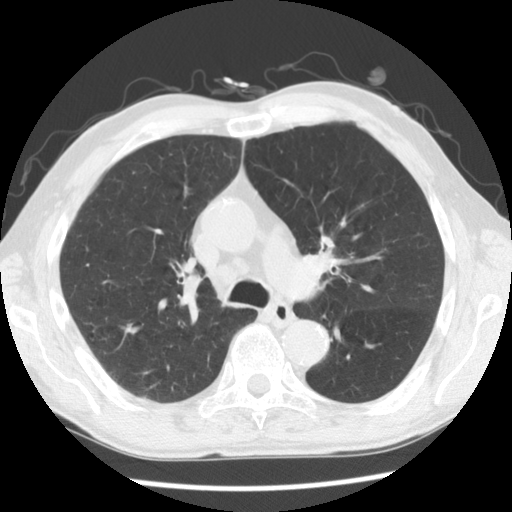
Low-dose screening chest CT, axial slice, baseline annual screen, lung window (W 1500 / L -600 HU), slice 83 of 132 in the series. Male participant, aged 68 years at enrolment. Current smoker at enrolment.
Expert reader's lesion annotation, box from (x=302, y=220) to (x=356, y=280) px. No non-calcified nodule or mass ≥4 mm was recorded by the screening reader at this exam. Official screen result: negative screen, minor abnormalities not suspicious for lung cancer. Lung cancer was diagnosed 215 days after this screen: squamous cell carcinoma, NOS, left hilum, stage IIB (AJCC 6th edition), 32 mm at pathology.